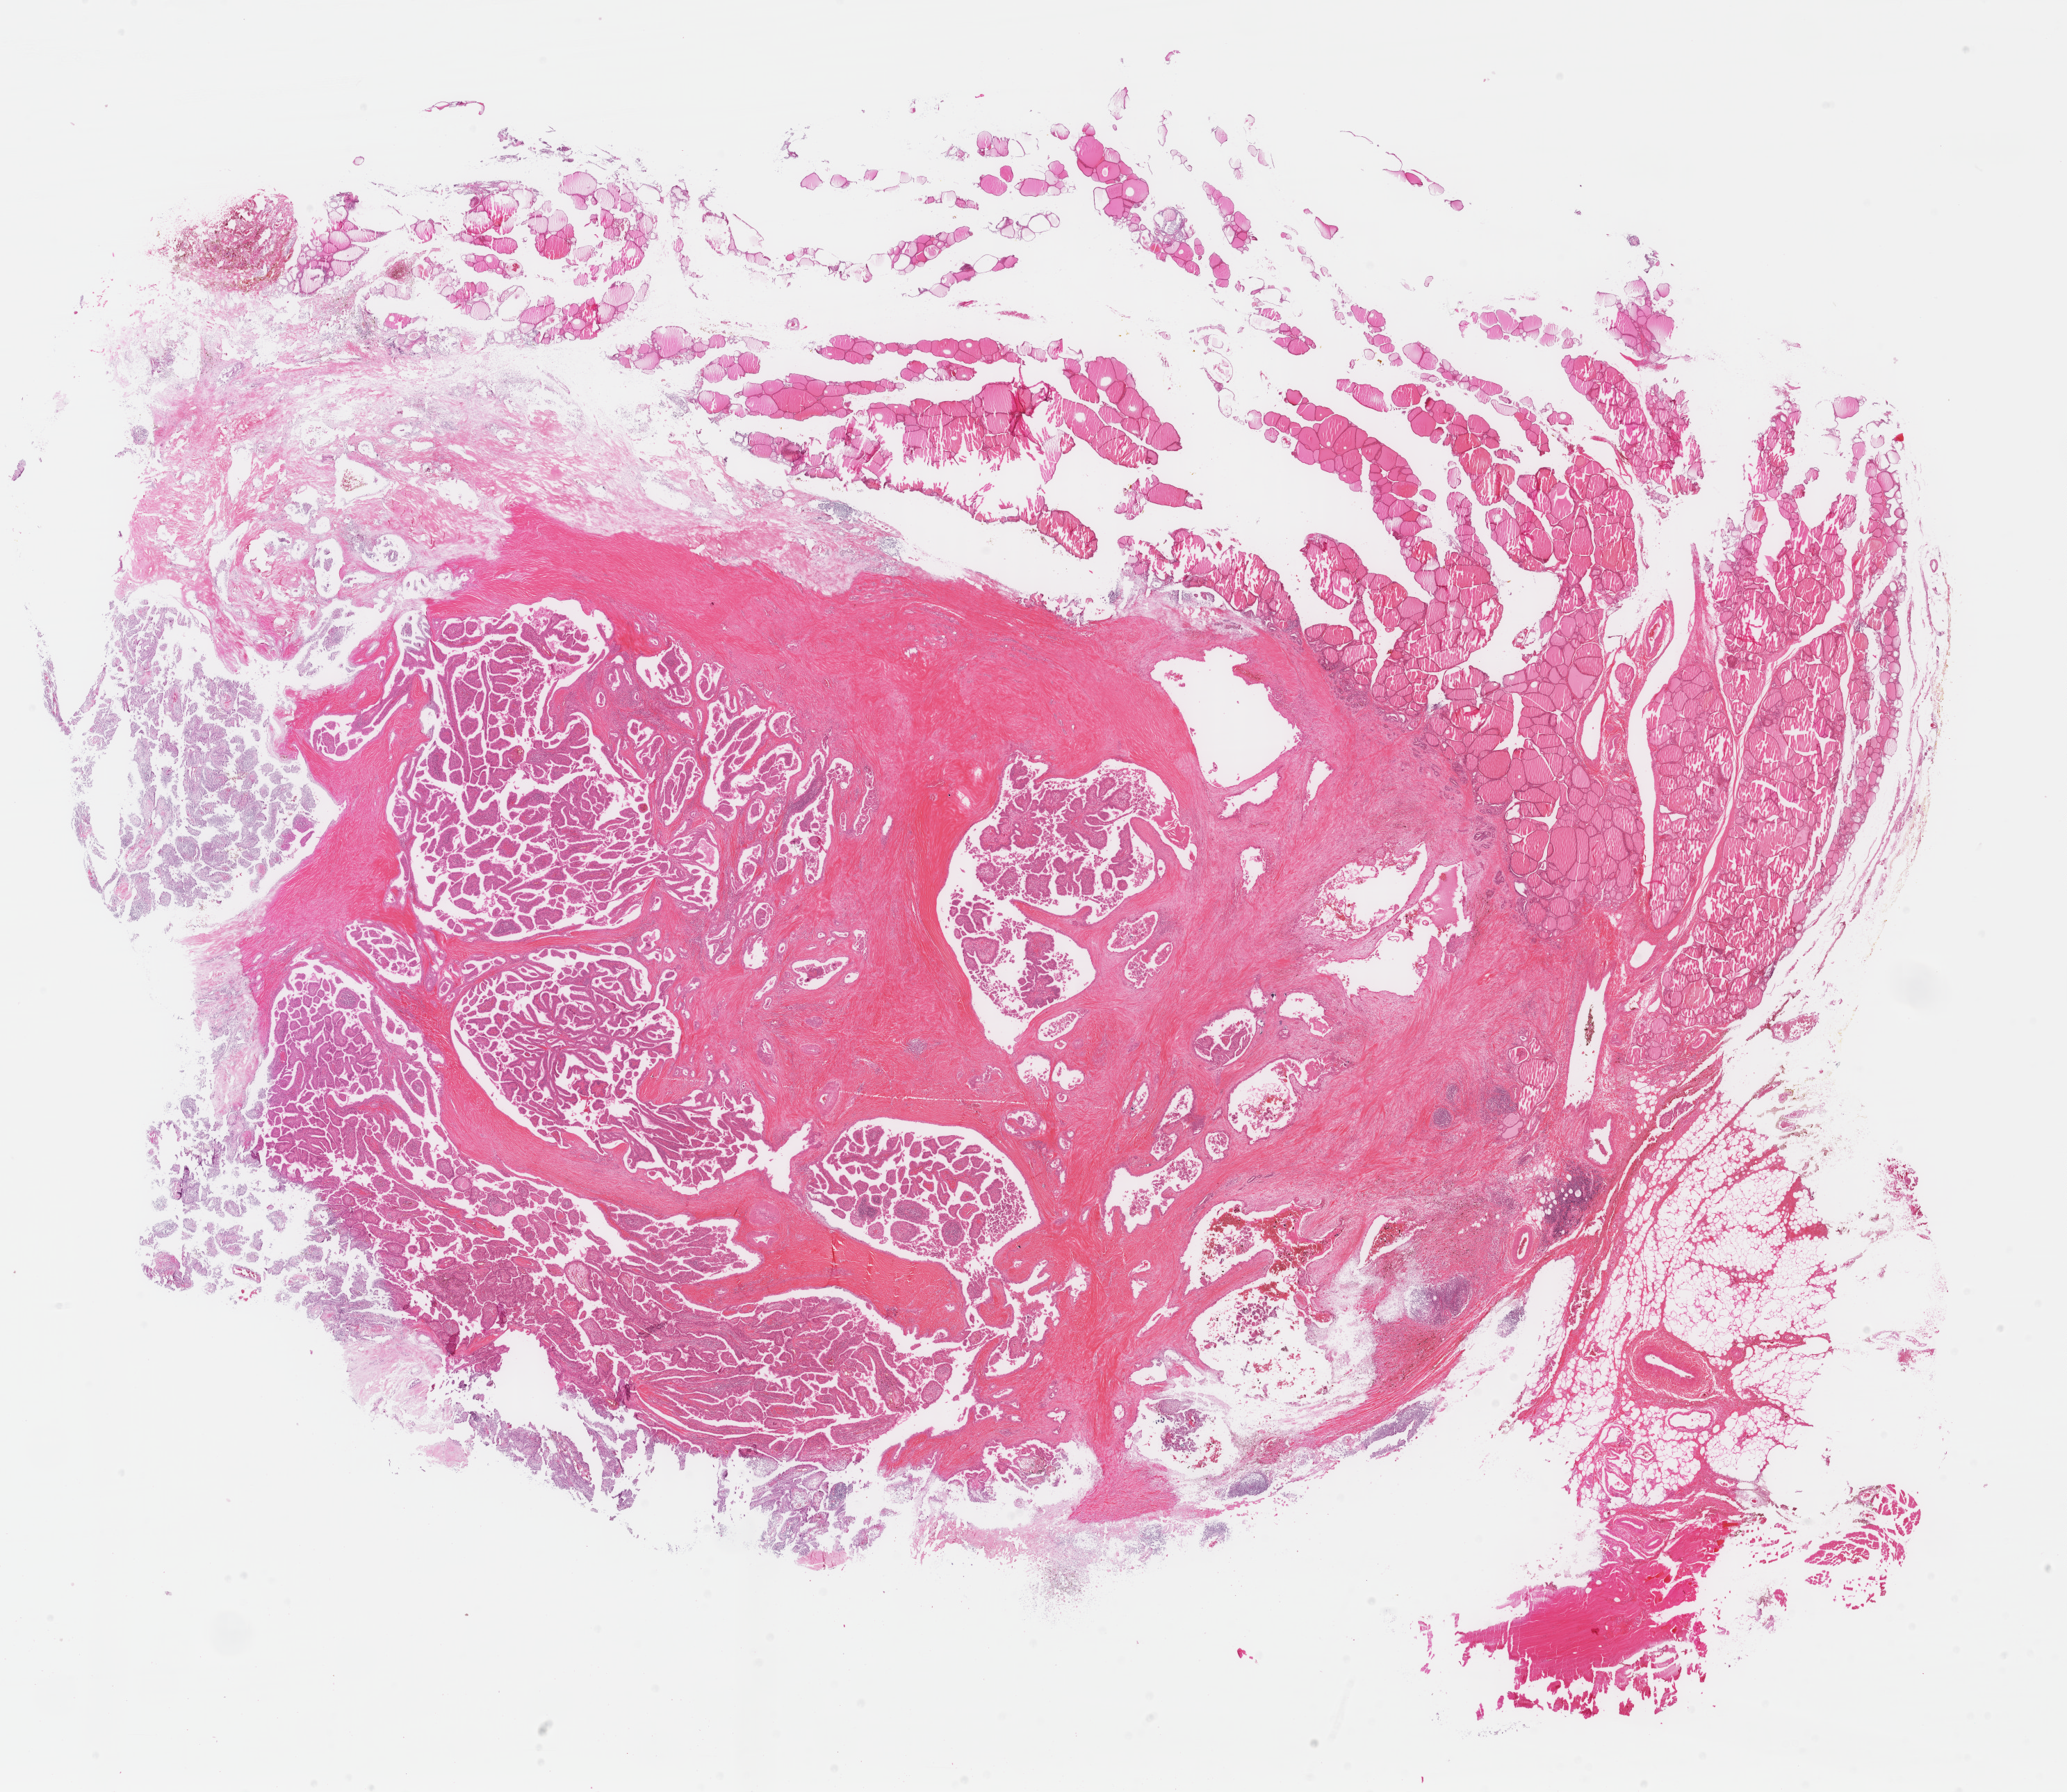
H&E-stained whole-slide image — low-resolution overview of the scanned area, about 23.6 x 20.5 mm. Formalin-fixed paraffin-embedded (FFPE) diagnostic section. Primary tumour sample from the thyroid. Patient: female, age at initial diagnosis 51 years.
Histologic diagnosis: Papillary adenocarcinoma, NOS (thyroid gland).